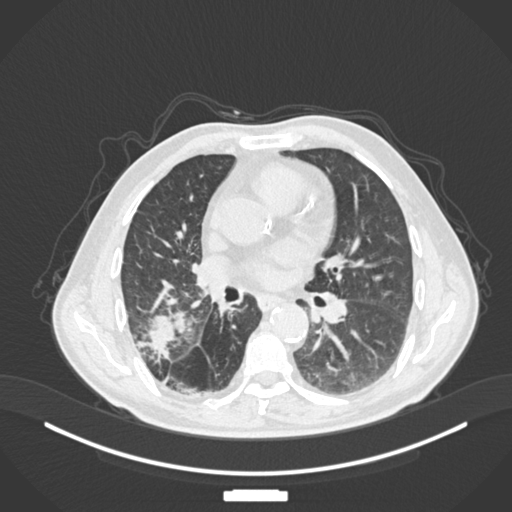
Chest CT, one axial slice; position 83 of 201 along the scan axis; 120 kVp; lung window (W 1500 / L -600 HU); 512 × 512 image matrix, field of view 400 × 400 mm. Patient: male, 72 years. Case-level facts recorded for this patient, not image findings: clinical TNM (as recorded): T3 N2 M0.
Annotated regions visible in this slice (rectangle marked by the reading radiologist):
- lung tumour (recorded histology: adenocarcinoma): box from (x=142, y=309) to (x=184, y=358) px